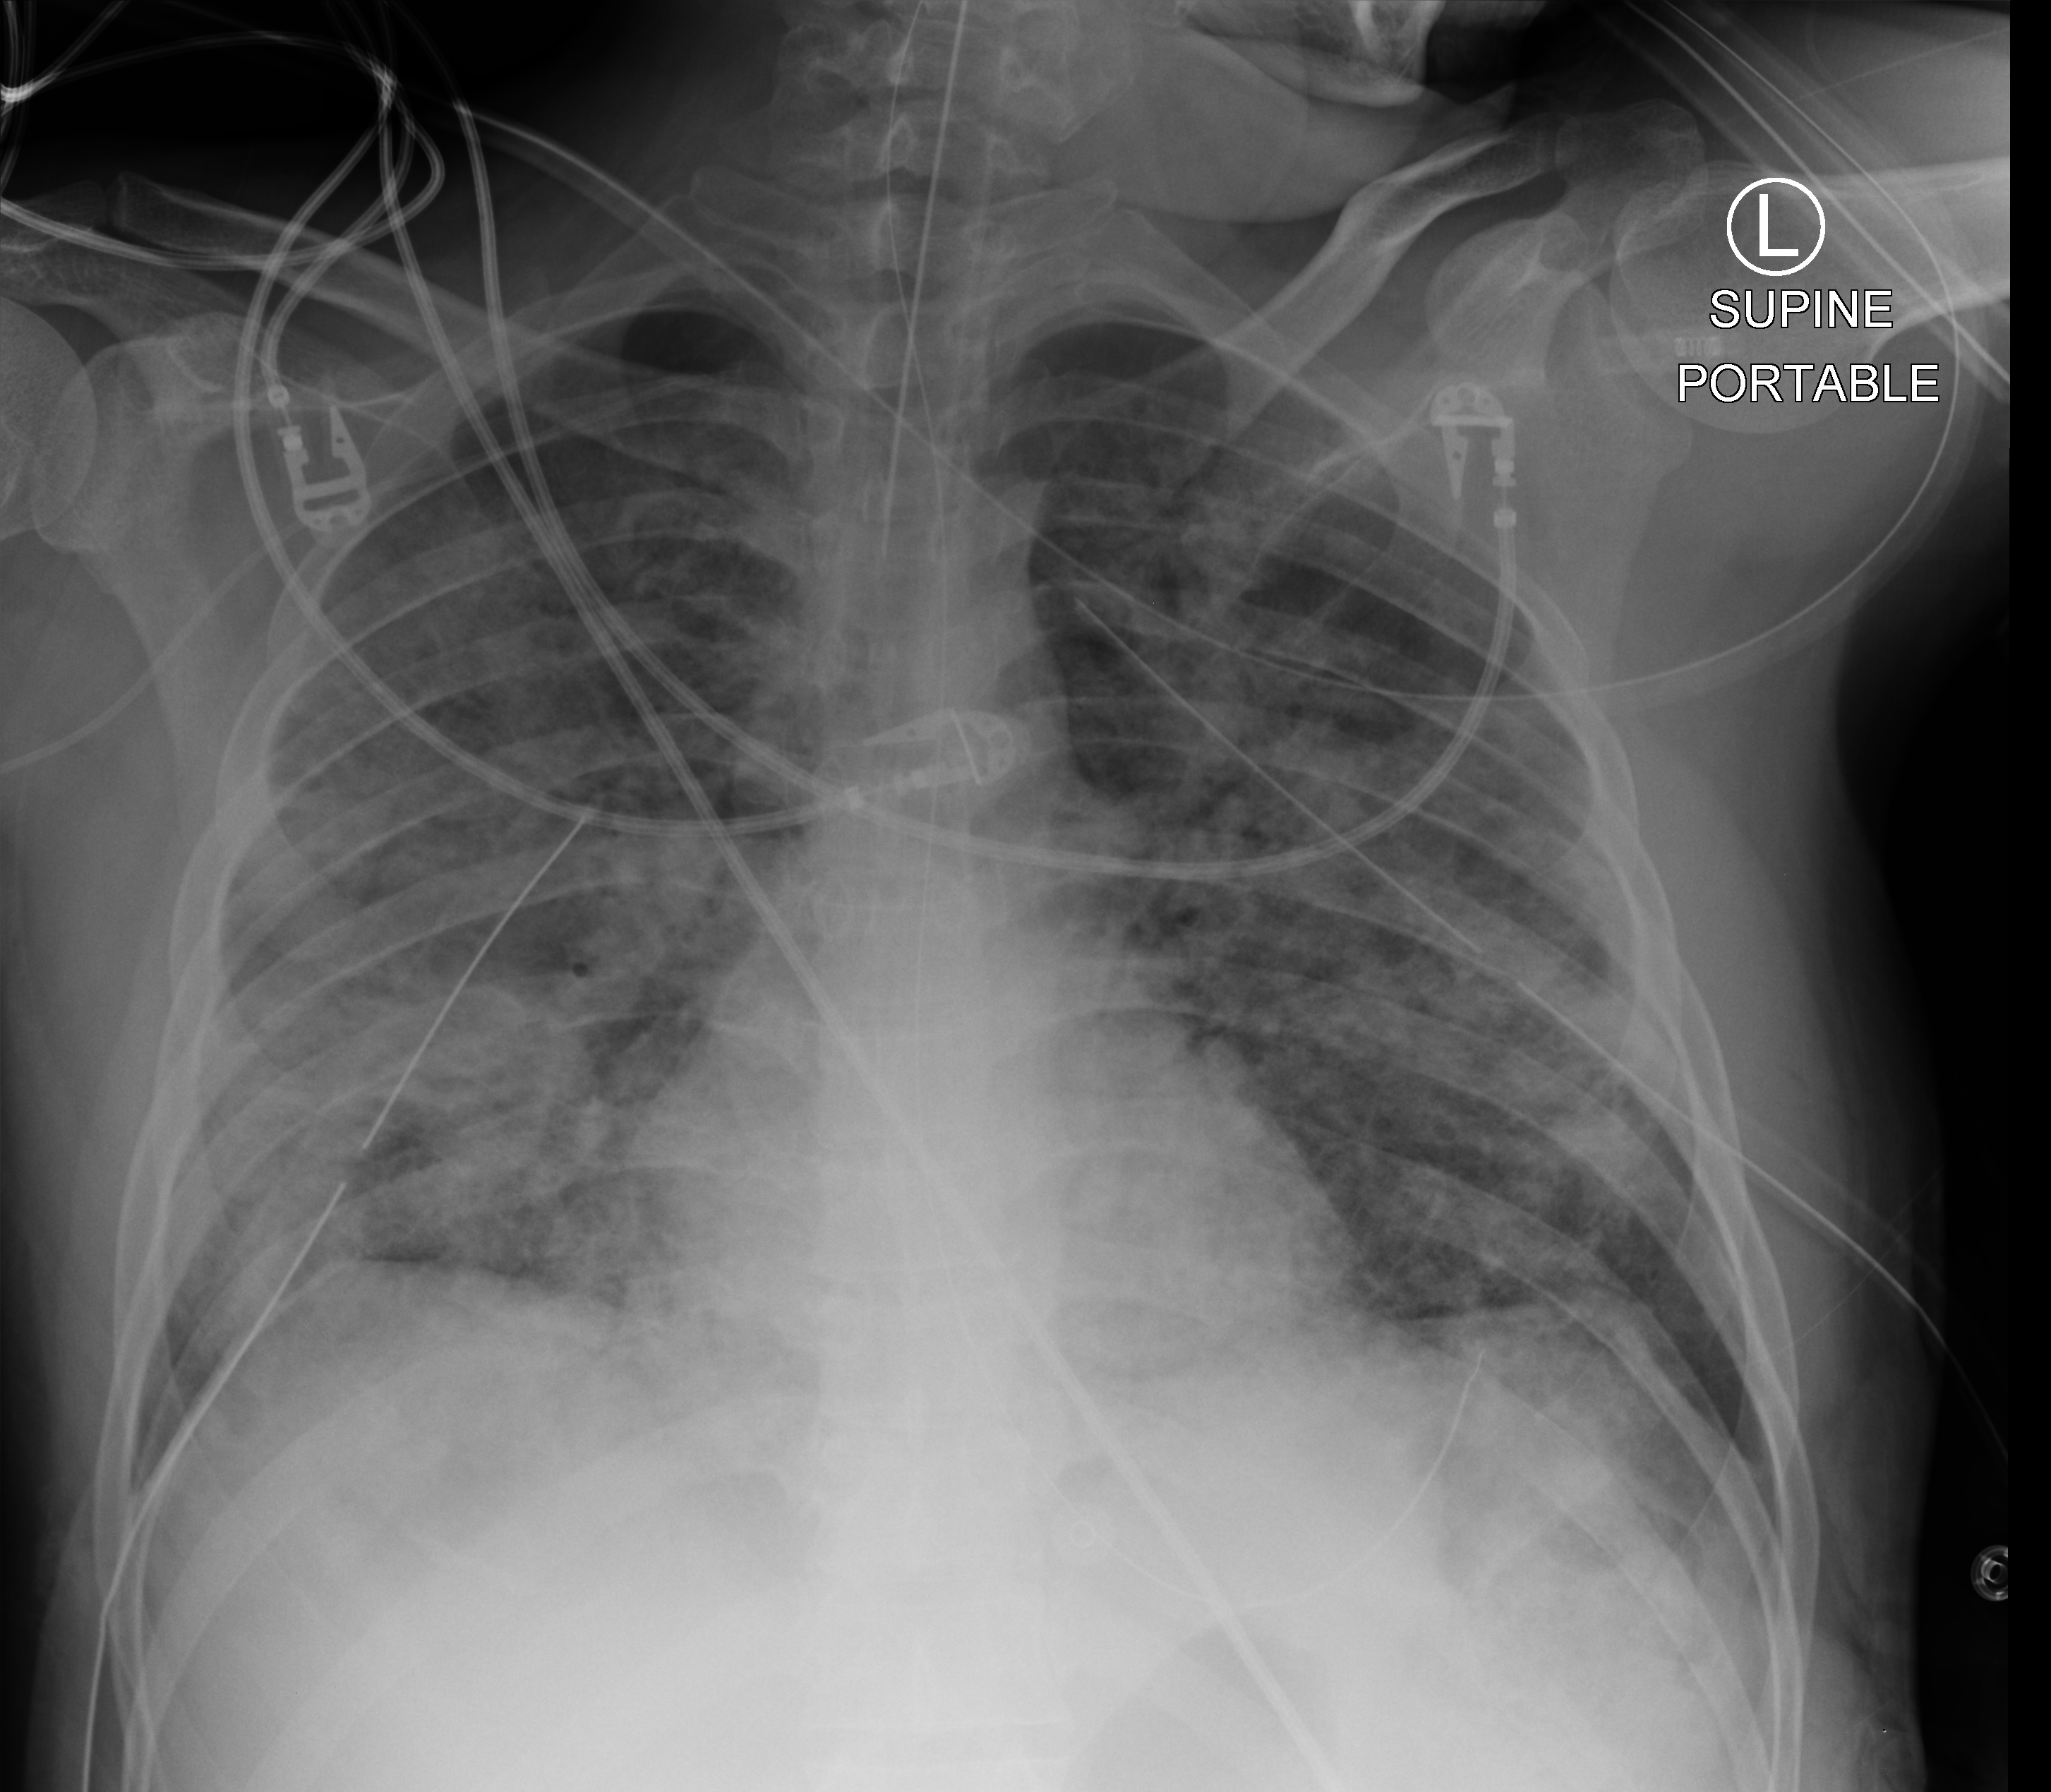
Bedside chest radiograph (computed radiography). Patient hospitalised with COVID-19; male, aged 18–59 years.
Admission-level facts for this patient (not findings on this image; timing relative to this image not recorded): mechanically ventilated during this hospital stay: yes.